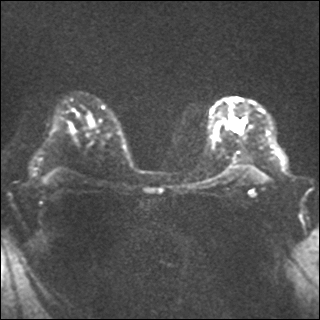
Breast MRI, one axial slice. Slice 24 of 35 in the series (ordered by position). Diffusion-weighted series; image 2 of 4 stored at this slice position (different b-values; order by instance number). 1.5 T. 4 mm slice thickness. 320 × 320 image matrix, field of view 320 × 320 mm. Female patient.
Structures marked on this image (expert manual segmentation):
- tumour on diffusion-weighted imaging: bounding box (x1, y1, x2, y2) in pixels: (231, 119, 243, 131)